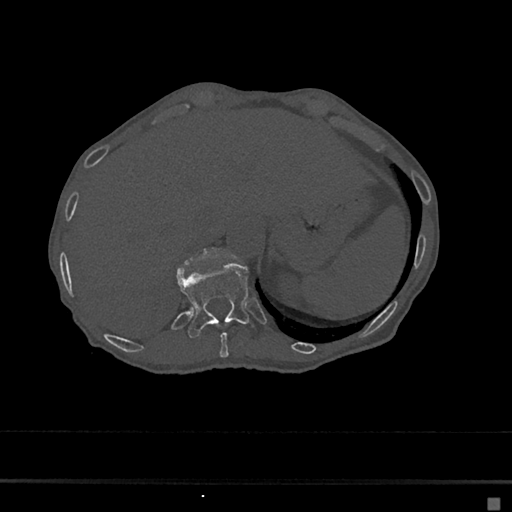
CT including the spine, one axial slice; position 182 of 797 along the scan axis; reconstruction kernel Br40s/3; bone window (W 1800 / L 400 HU); 0.5 mm slice thickness; 512 × 512 image matrix, field of view 360 × 360 mm. Patient: female, 68 years. Case-level facts recorded for this patient, not image findings: primary cancer: renal.
Annotated regions visible in this slice (semi-automatically segmented with operator editing):
- T10 vertebra: bounding box (x1, y1, x2, y2) in pixels: (216, 324, 228, 357)
- T11 vertebra: (176, 263, 252, 339)
- T12 vertebra: (182, 250, 212, 267)